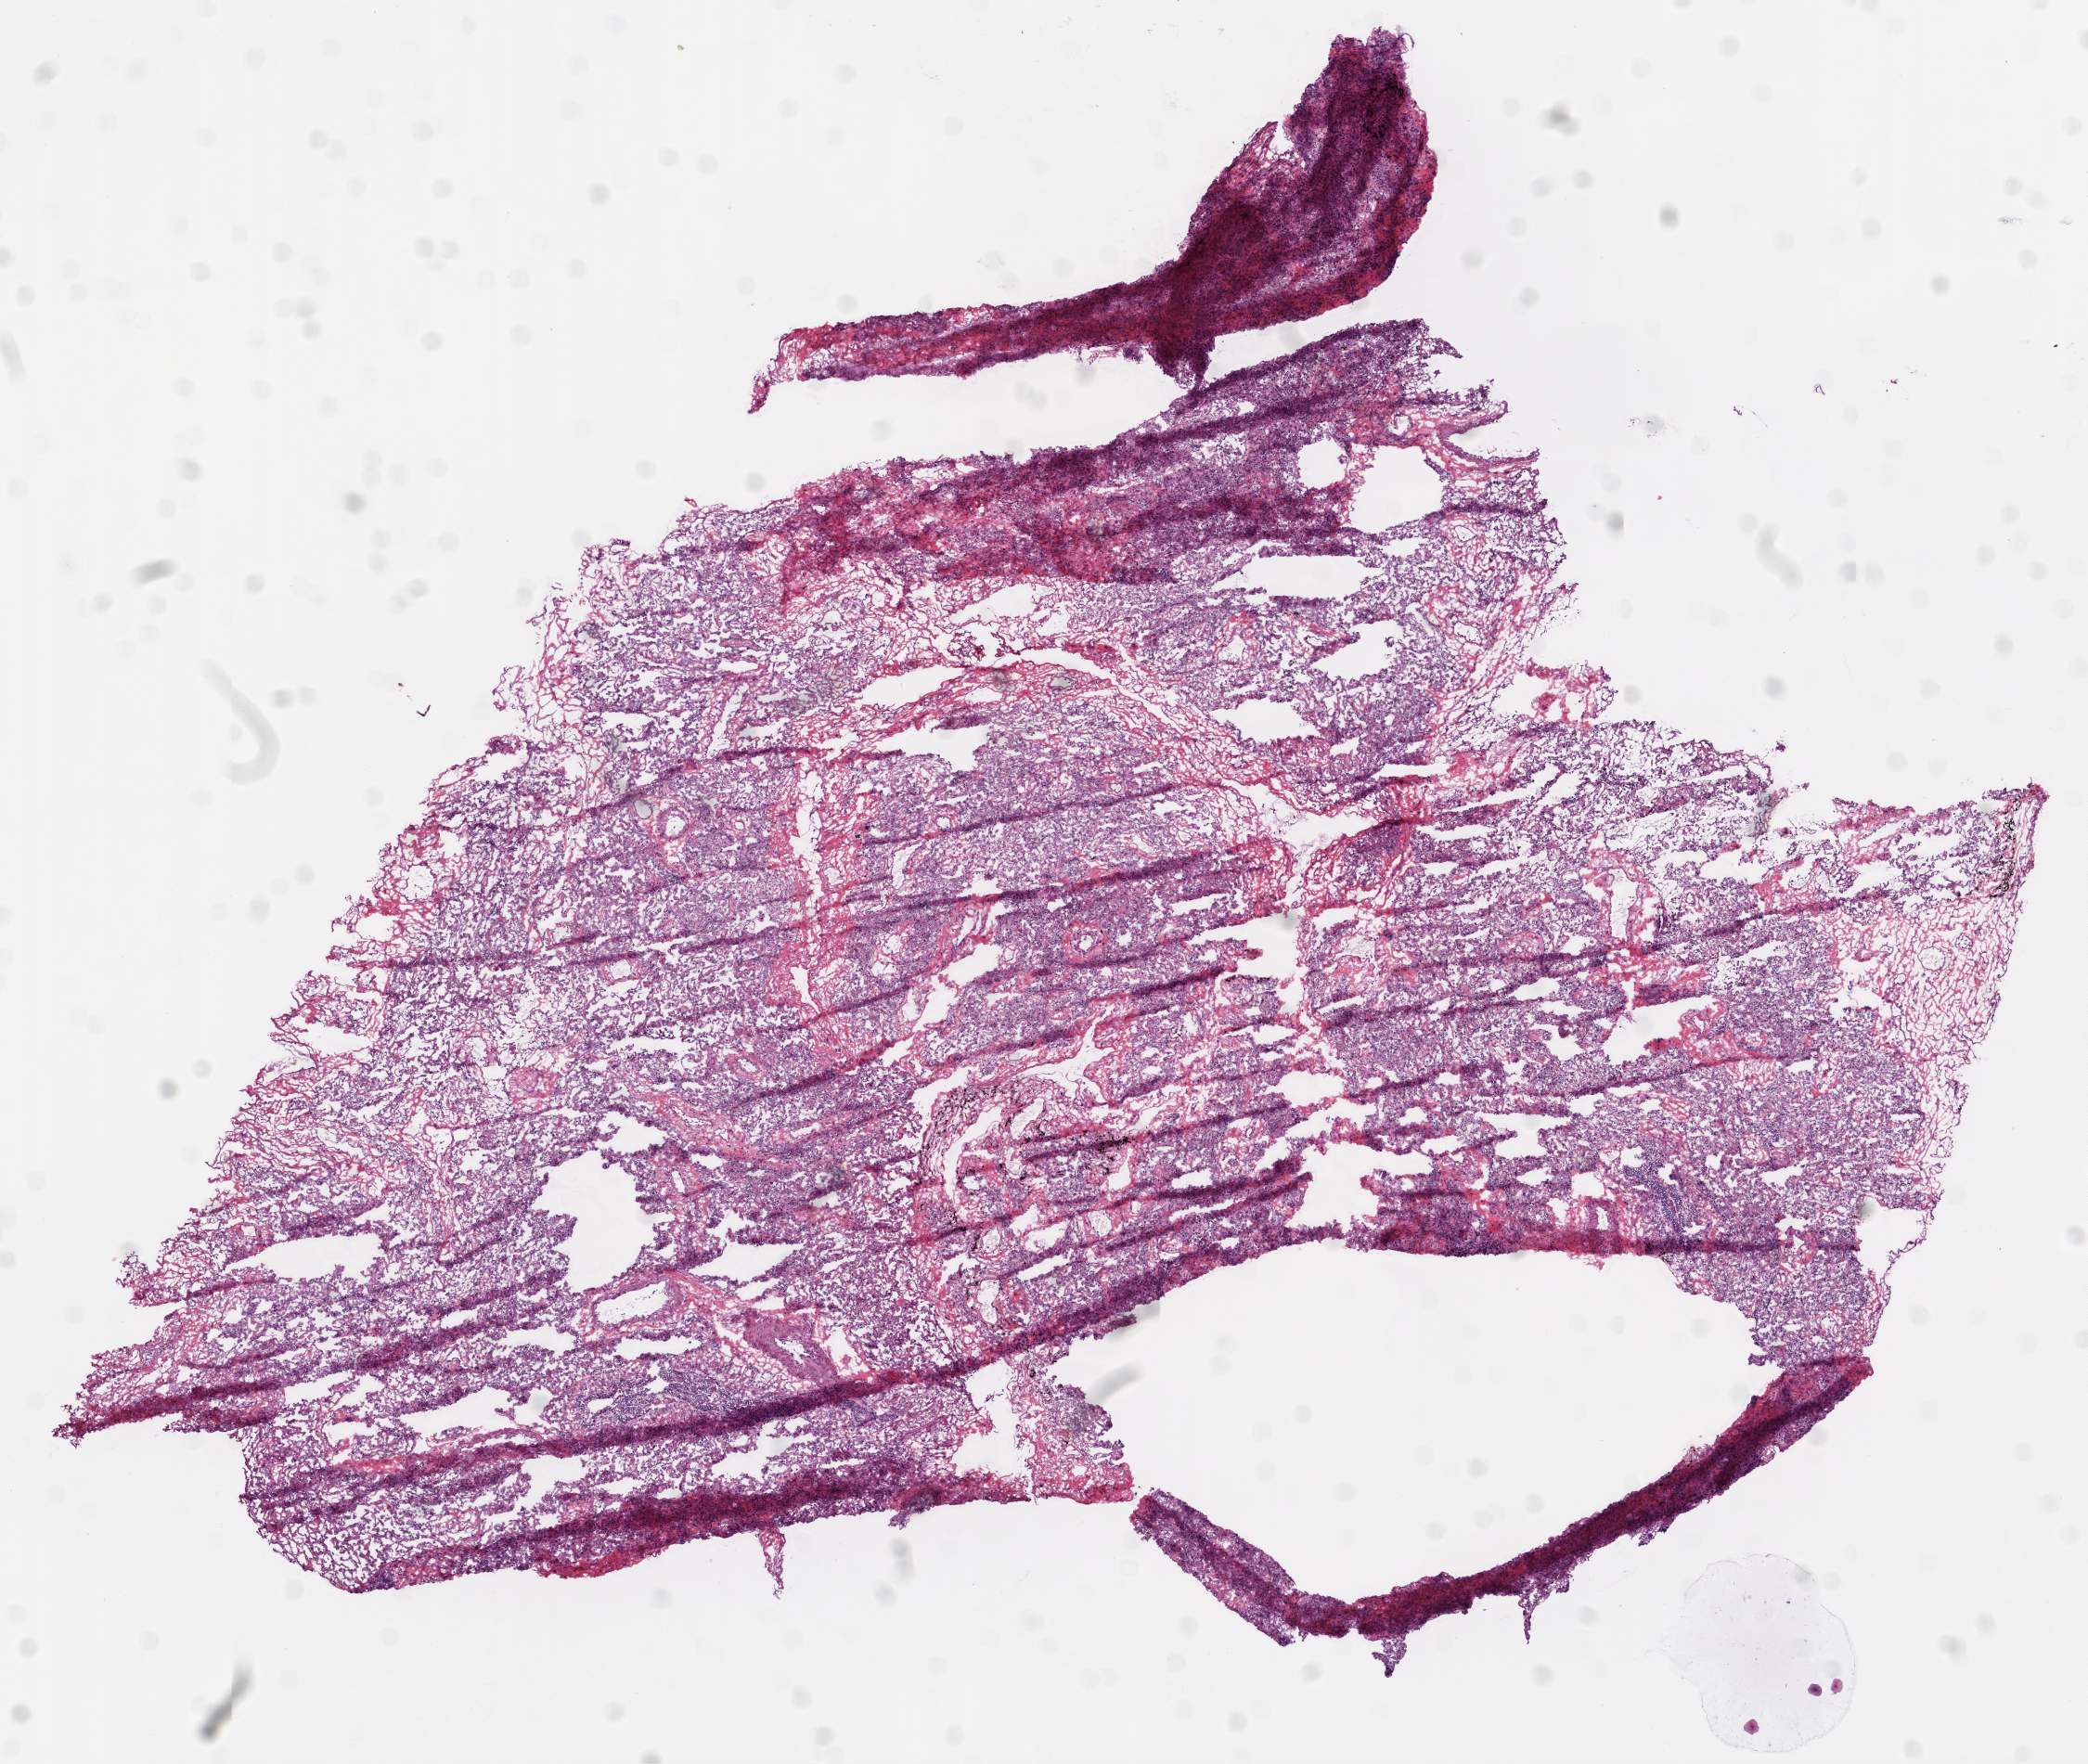
Whole-slide histology image, H&E-stained — shown as a low-resolution overview of the whole scanned area (about 9.0 x 7.6 mm), frozen section from the top of the tissue portion, sample: solid tissue normal (non-tumour tissue), lung. Male patient; age at initial diagnosis 57 years.
This section: solid tissue normal (non-tumour) sample from the same patient. Patient diagnosis: Squamous cell carcinoma, NOS.